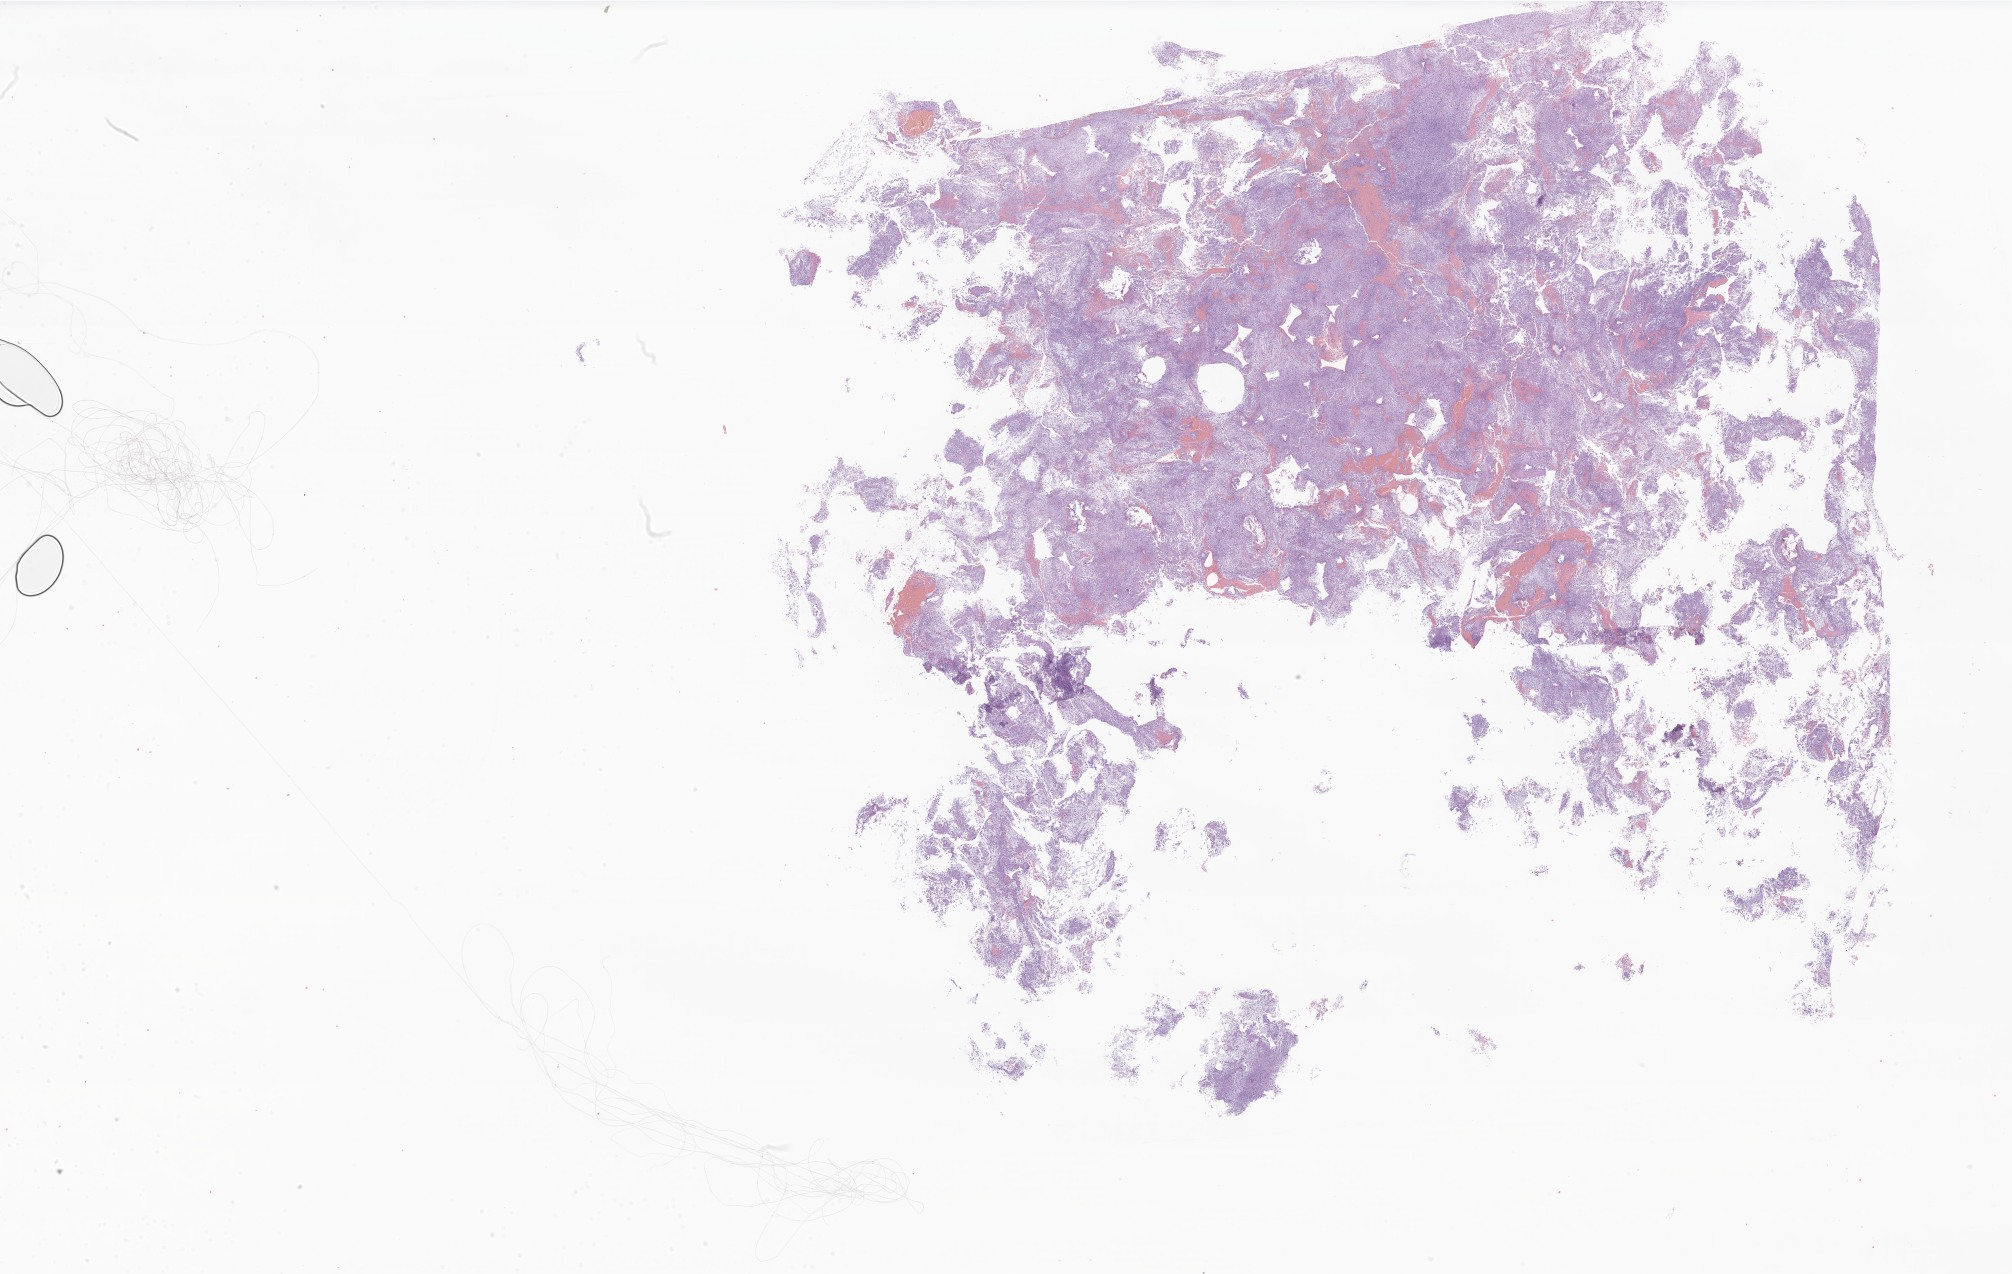
Hematoxylin and eosin (H&E) whole-slide image of tumor tissue from the brain, low-resolution overview of the scanned area, about 33.9 x 21.5 mm; FFPE section. Patient female; age 145 months (12 years 1 month).
• diagnosis: Neoplasm, malignant